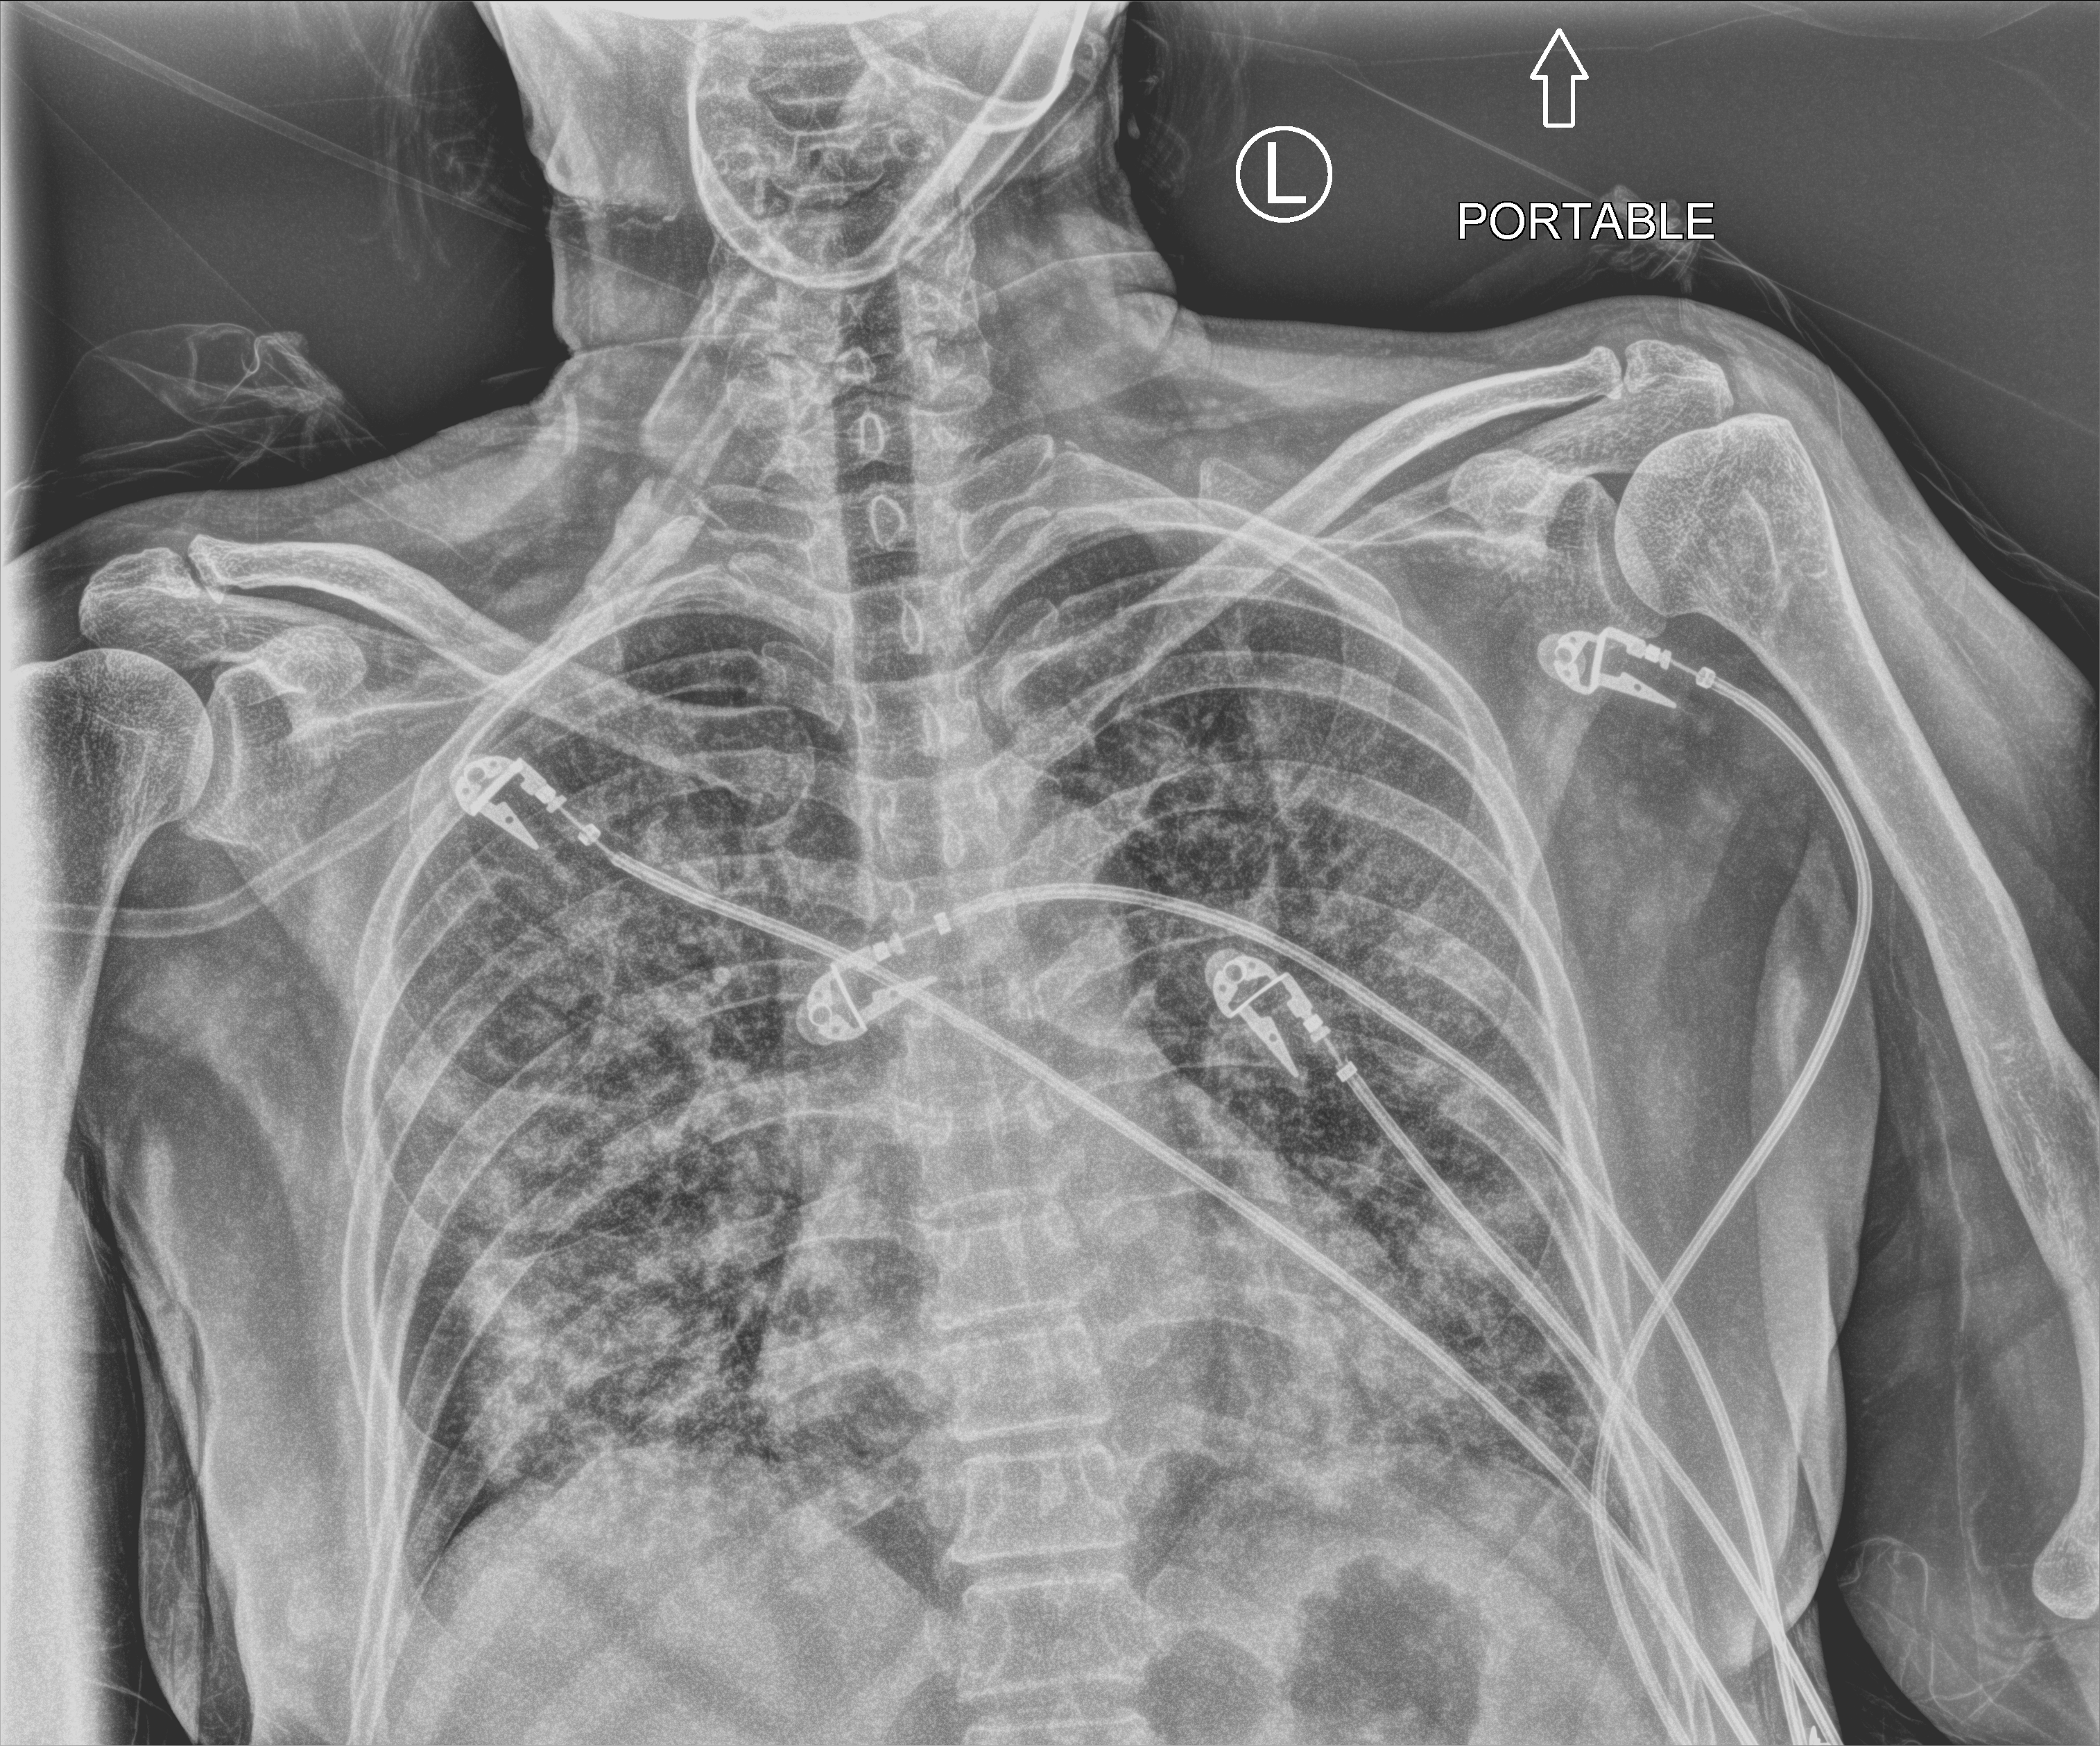
Portable chest radiograph; anteroposterior (AP) projection. Patient hospitalised with COVID-19; female, aged 60–74 years.
Hospital-stay facts (about this admission, not read from this image; timing relative to this image not recorded): chronic kidney disease (admission record): no; mechanically ventilated during this hospital stay: no.